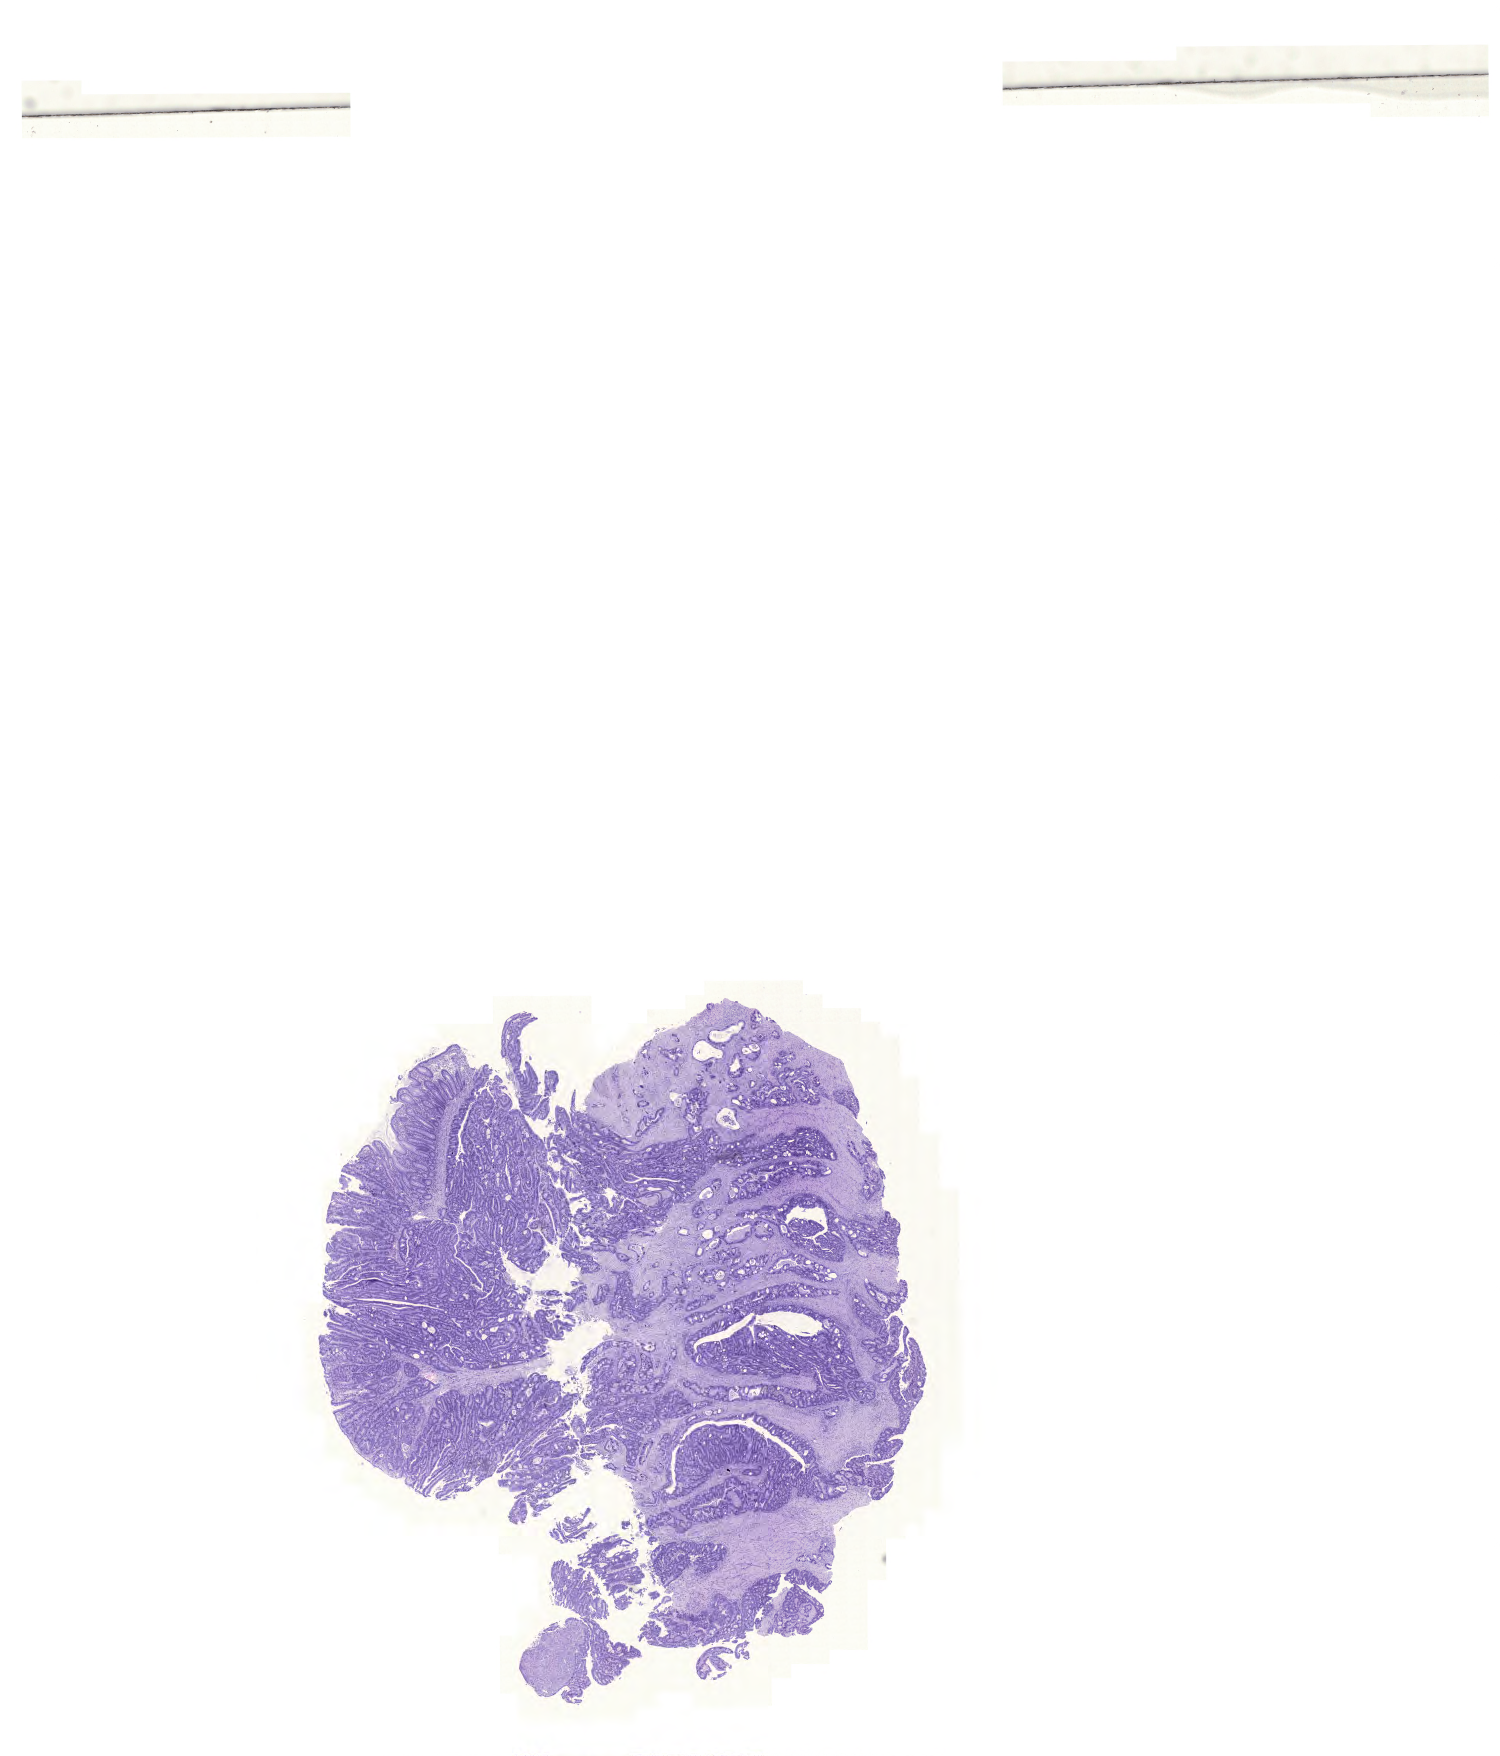
Digitized Hematoxylin and eosin (H&E) stained tissue section (whole slide), whole scanned area (about 22.3 x 26.1 mm, slide scanned at 20x) shown as a low-resolution overview; FFPE section; sample: primary tumour, colon. Female, age 84 years at initial diagnosis.
AJCC pathologic stage: IVA (7th edition). Diagnosis: Adenocarcinoma, NOS. TNM: T4 N1b M1a. Lymph nodes positive (case pathology): 3 of 41 examined.